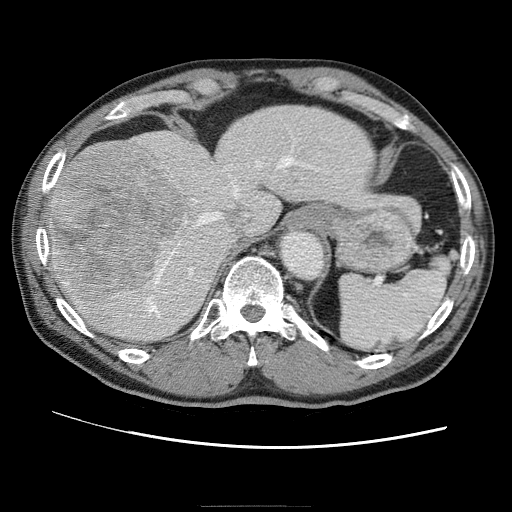
Contrast-enhanced abdominal CT (liver protocol), one axial slice; slice 46 of 75 in the series (ordered by position); reconstruction kernel STANDARD; one of 2 acquisitions stored at this slice position; soft-tissue window (W 400 / L 40 HU); 2.5 mm slice thickness; 512 × 512 image matrix, field of view 360 × 360 mm. From the clinical record (not read from this slice): diagnosis: hepatocellular carcinoma (patient treated with transarterial chemoembolisation; whether this scan precedes or follows treatment is not stated here); TNM stage (as recorded): Stage-II; Child-Pugh class: A; tumour differentiation: well differentiated; tumour nodularity: multinodular.
Structures marked on this image (semi-automatic segmentation, software-assisted and operator-edited):
- abdominal aorta: bounding box [x1, y1, x2, y2] px = [279, 231, 322, 278]
- liver parenchyma outside the tumour (the mass and vessels are separate outlines, so this box may not span the whole liver): [48, 106, 376, 342]
- mass: [49, 145, 187, 298]
- liver vessels: [137, 152, 277, 305]